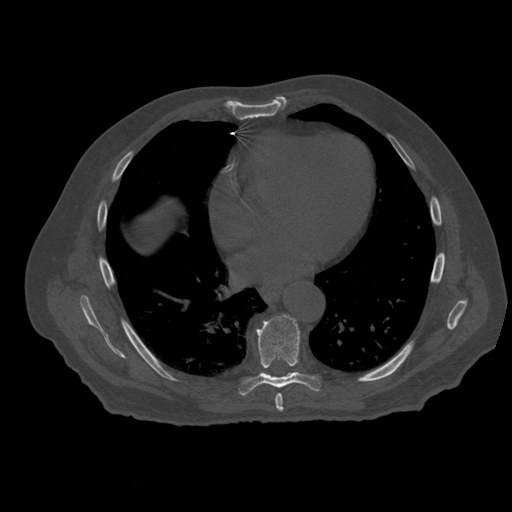
CT including the spine, one axial slice. Position 343 of 399 along the scan axis. Reconstruction kernel STANDARD. 120 kVp. Bone window (W 1800 / L 400 HU). 512 × 512 image matrix, field of view 407 × 407 mm. Patient age 73 years. Case-level facts recorded for this patient, not image findings: primary cancer: prostate; vertebrae with lytic lesions (as recorded): L2.
Outlined on this slice (semi-automatically segmented with operator editing):
- T7 vertebra: box from (x=276, y=394) to (x=284, y=413) px
- T8 vertebra: (x=239, y=315)–(x=322, y=396)